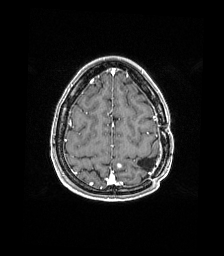
Brain MRI from a brain-tumour surgery series, one axial slice; position 45 of 176 along the scan axis; T1-weighted post-contrast; 1 mm slice thickness; 224 × 256 image matrix, field of view 224 × 256 mm. Case-level facts recorded for this patient, not image findings: histopathology: Atypical meningioma; WHO grade: 2; tumour location: Paramedian Left Parietal.
Structures marked on this image (manually delineated by an expert):
- previous resection cavity: bounding box [x1, y1, x2, y2] px = [137, 157, 156, 171]
- tumour: [116, 162, 122, 169]